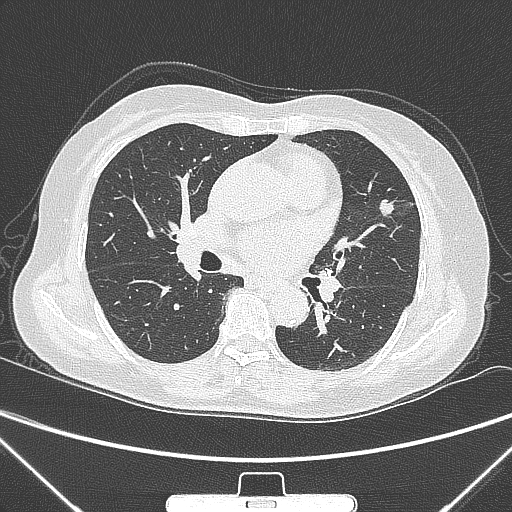
Chest CT, one axial slice; slice 148 of 300 in the series (ordered by position); lung window (W 1500 / L -600 HU); 512 × 512 image matrix. Female patient, age 70 years. From the clinical record (not read from this slice): clinical TNM (as recorded): T1b N0 M0; histopathological grade: G2.
Structures marked on this image (bounding box drawn by a radiologist):
- lung tumour (recorded histology: adenocarcinoma): bounding box (x1, y1, x2, y2) in pixels: (371, 193, 398, 227)